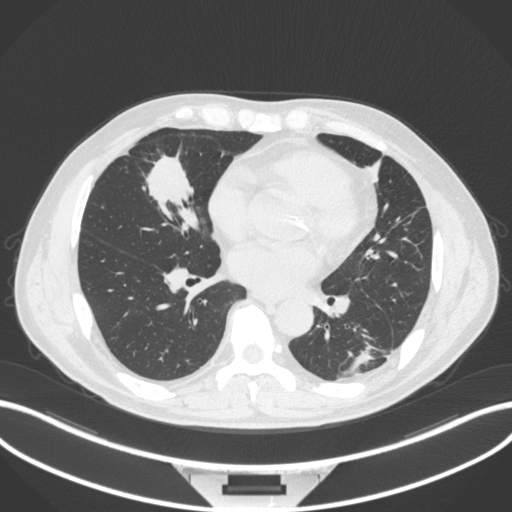
Chest CT, one axial slice; slice 128 of 399 in the series (ordered by position); reconstruction kernel B31f; 120 kVp; lung window (W 1500 / L -600 HU); 512 × 512 image matrix, field of view 400 × 400 mm. Patient: male, 59 years. From the clinical record (not read from this slice): clinical TNM (as recorded): T2a N1 M0.
Outlined on this slice (bounding box drawn by a radiologist):
- lung tumour (recorded histology: adenocarcinoma): box from (x=141, y=143) to (x=201, y=211) px